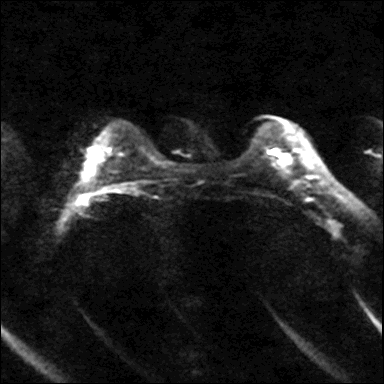
Breast MRI, one axial slice; slice 10 of 40 in the series (ordered by position); diffusion-weighted series; image 2 of 4 stored at this slice position (different b-values; order by instance number); 3 T; 4 mm slice thickness; 384 × 384 image matrix, field of view 320 × 320 mm. Female patient.
Outlined on this slice (manually delineated by an expert):
- tumour on diffusion-weighted imaging: bounding box [x1, y1, x2, y2] px = [282, 154, 287, 158]